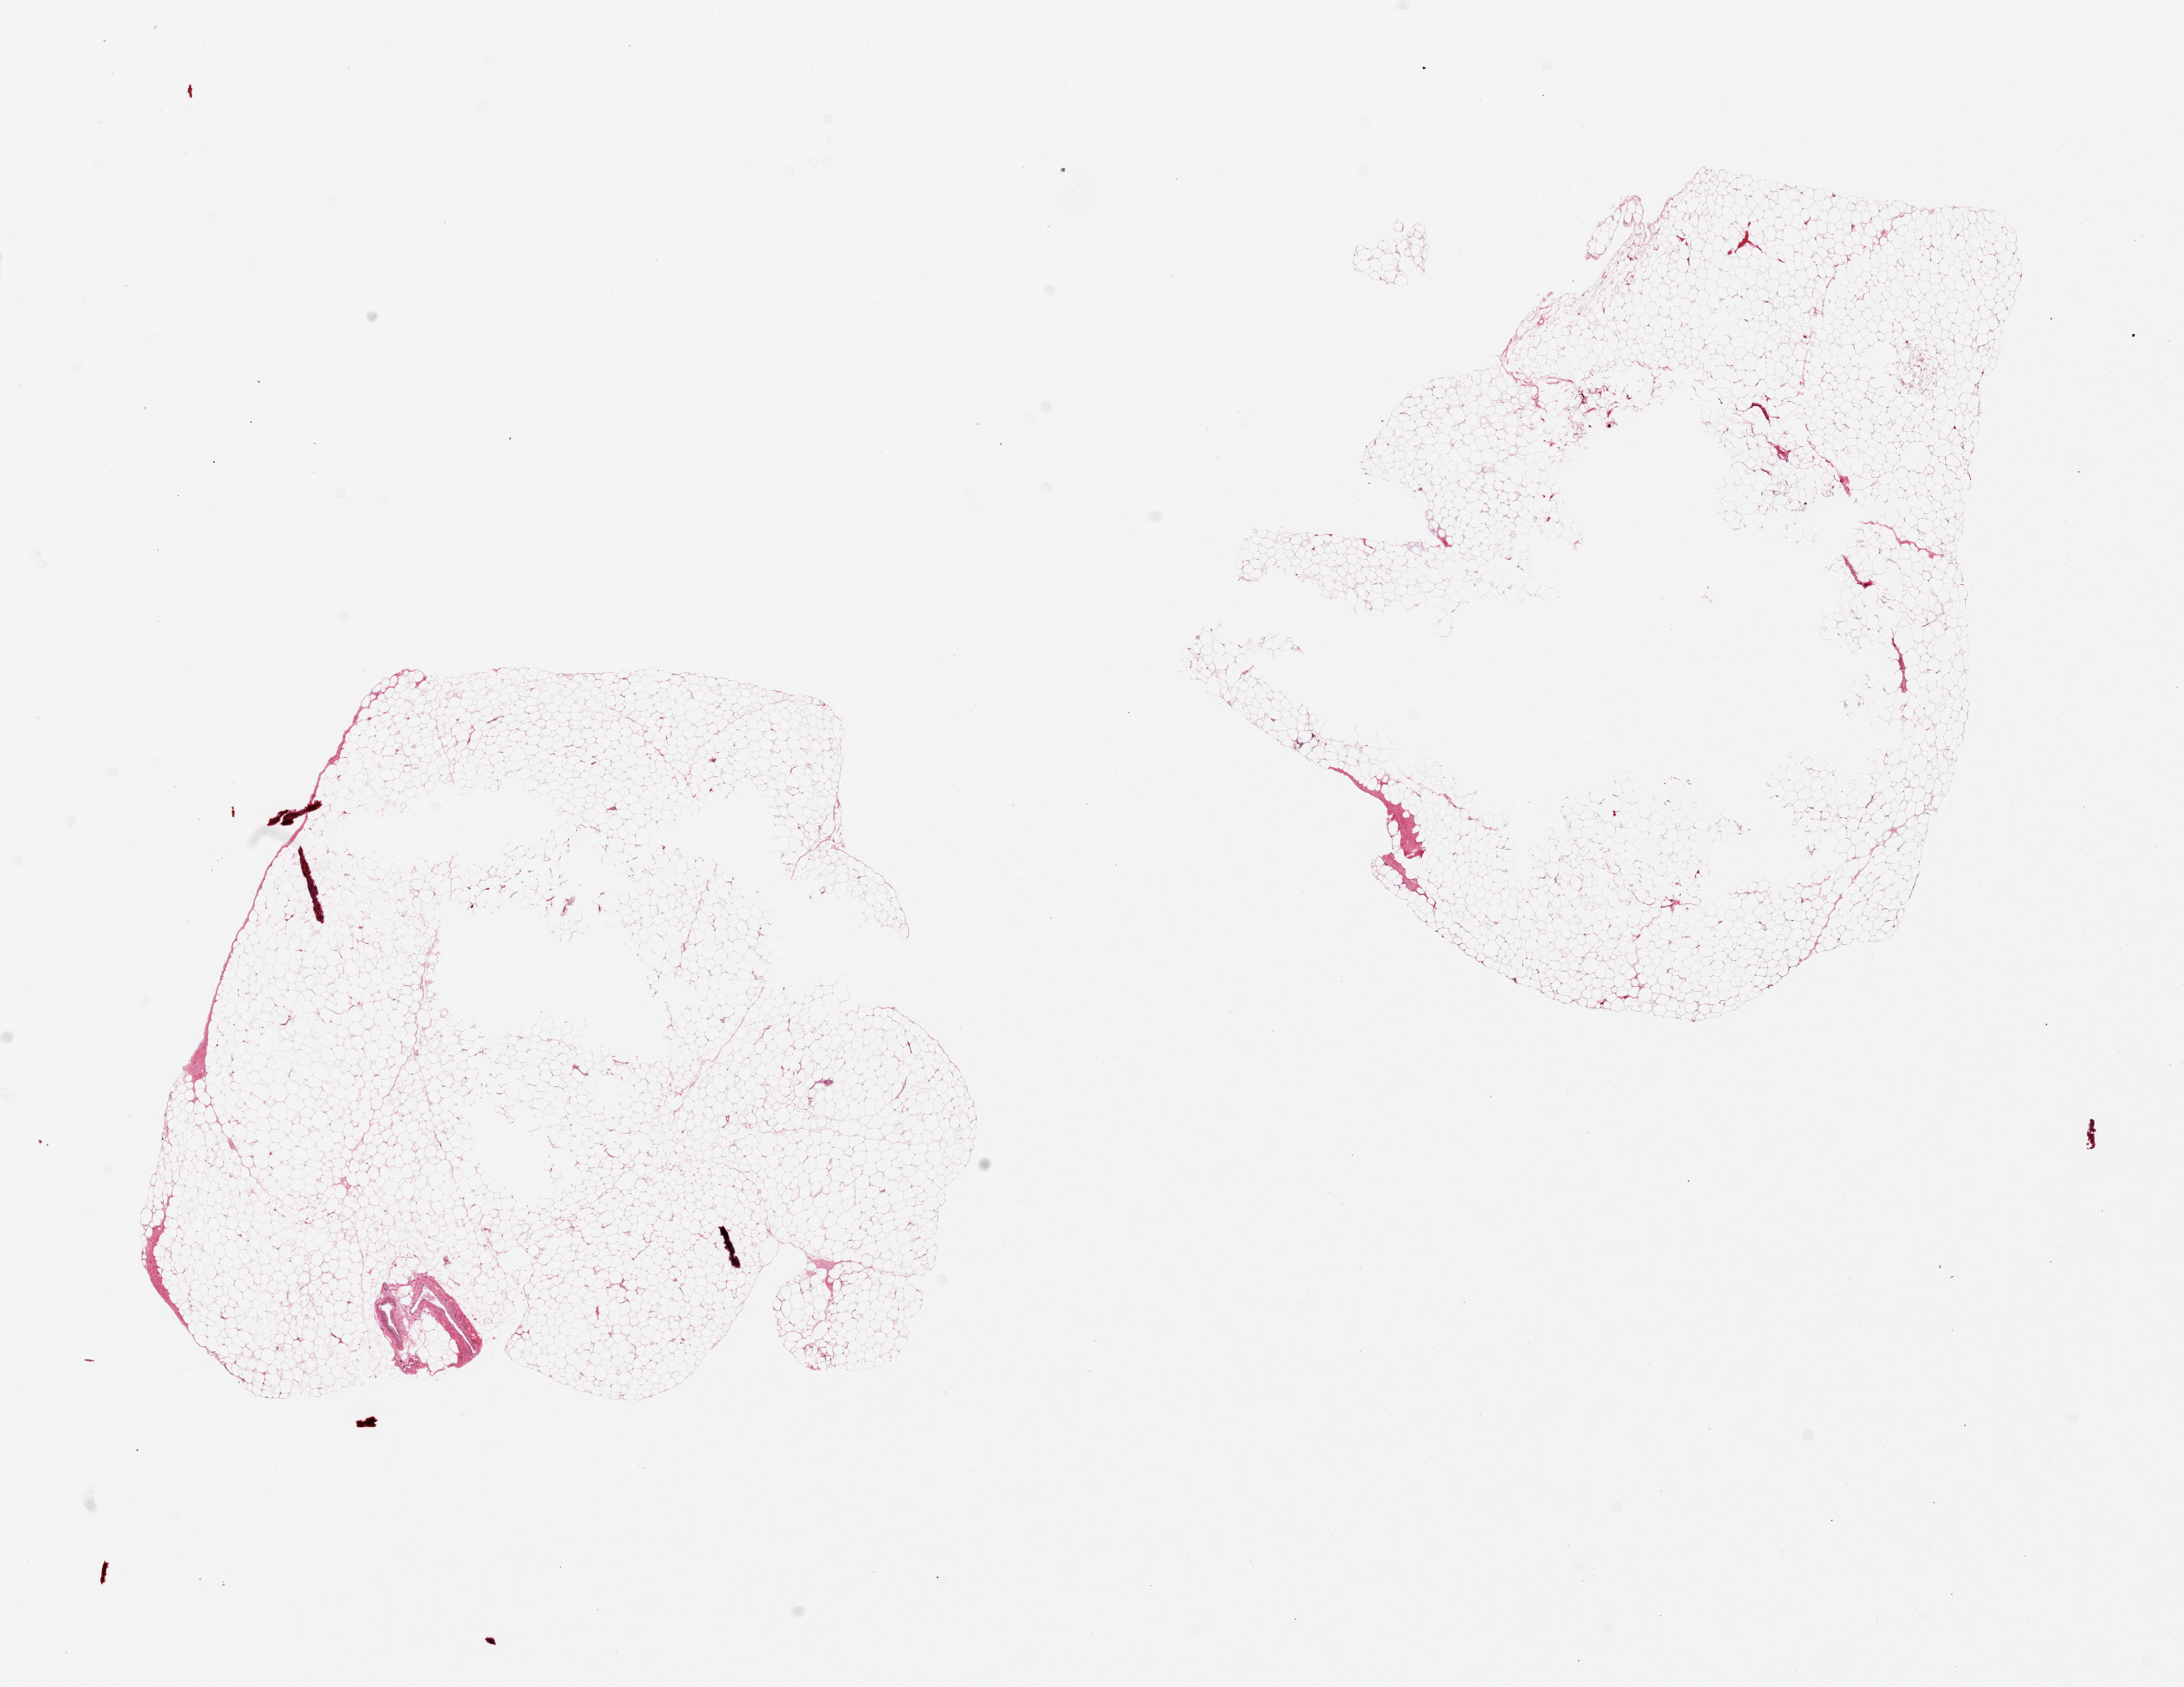
Whole-slide image, haematoxylin and eosin stain — a low-resolution overview of the entire scanned area, about 20.7 x 16.0 mm, PAXgene-fixed paraffin-embedded (PFPE) section, section of omentum (target tissue), donor tissue sample. Male donor.
• reviewer comment on this tissue sample: 2 pieces, no abnormality; prominent vessel